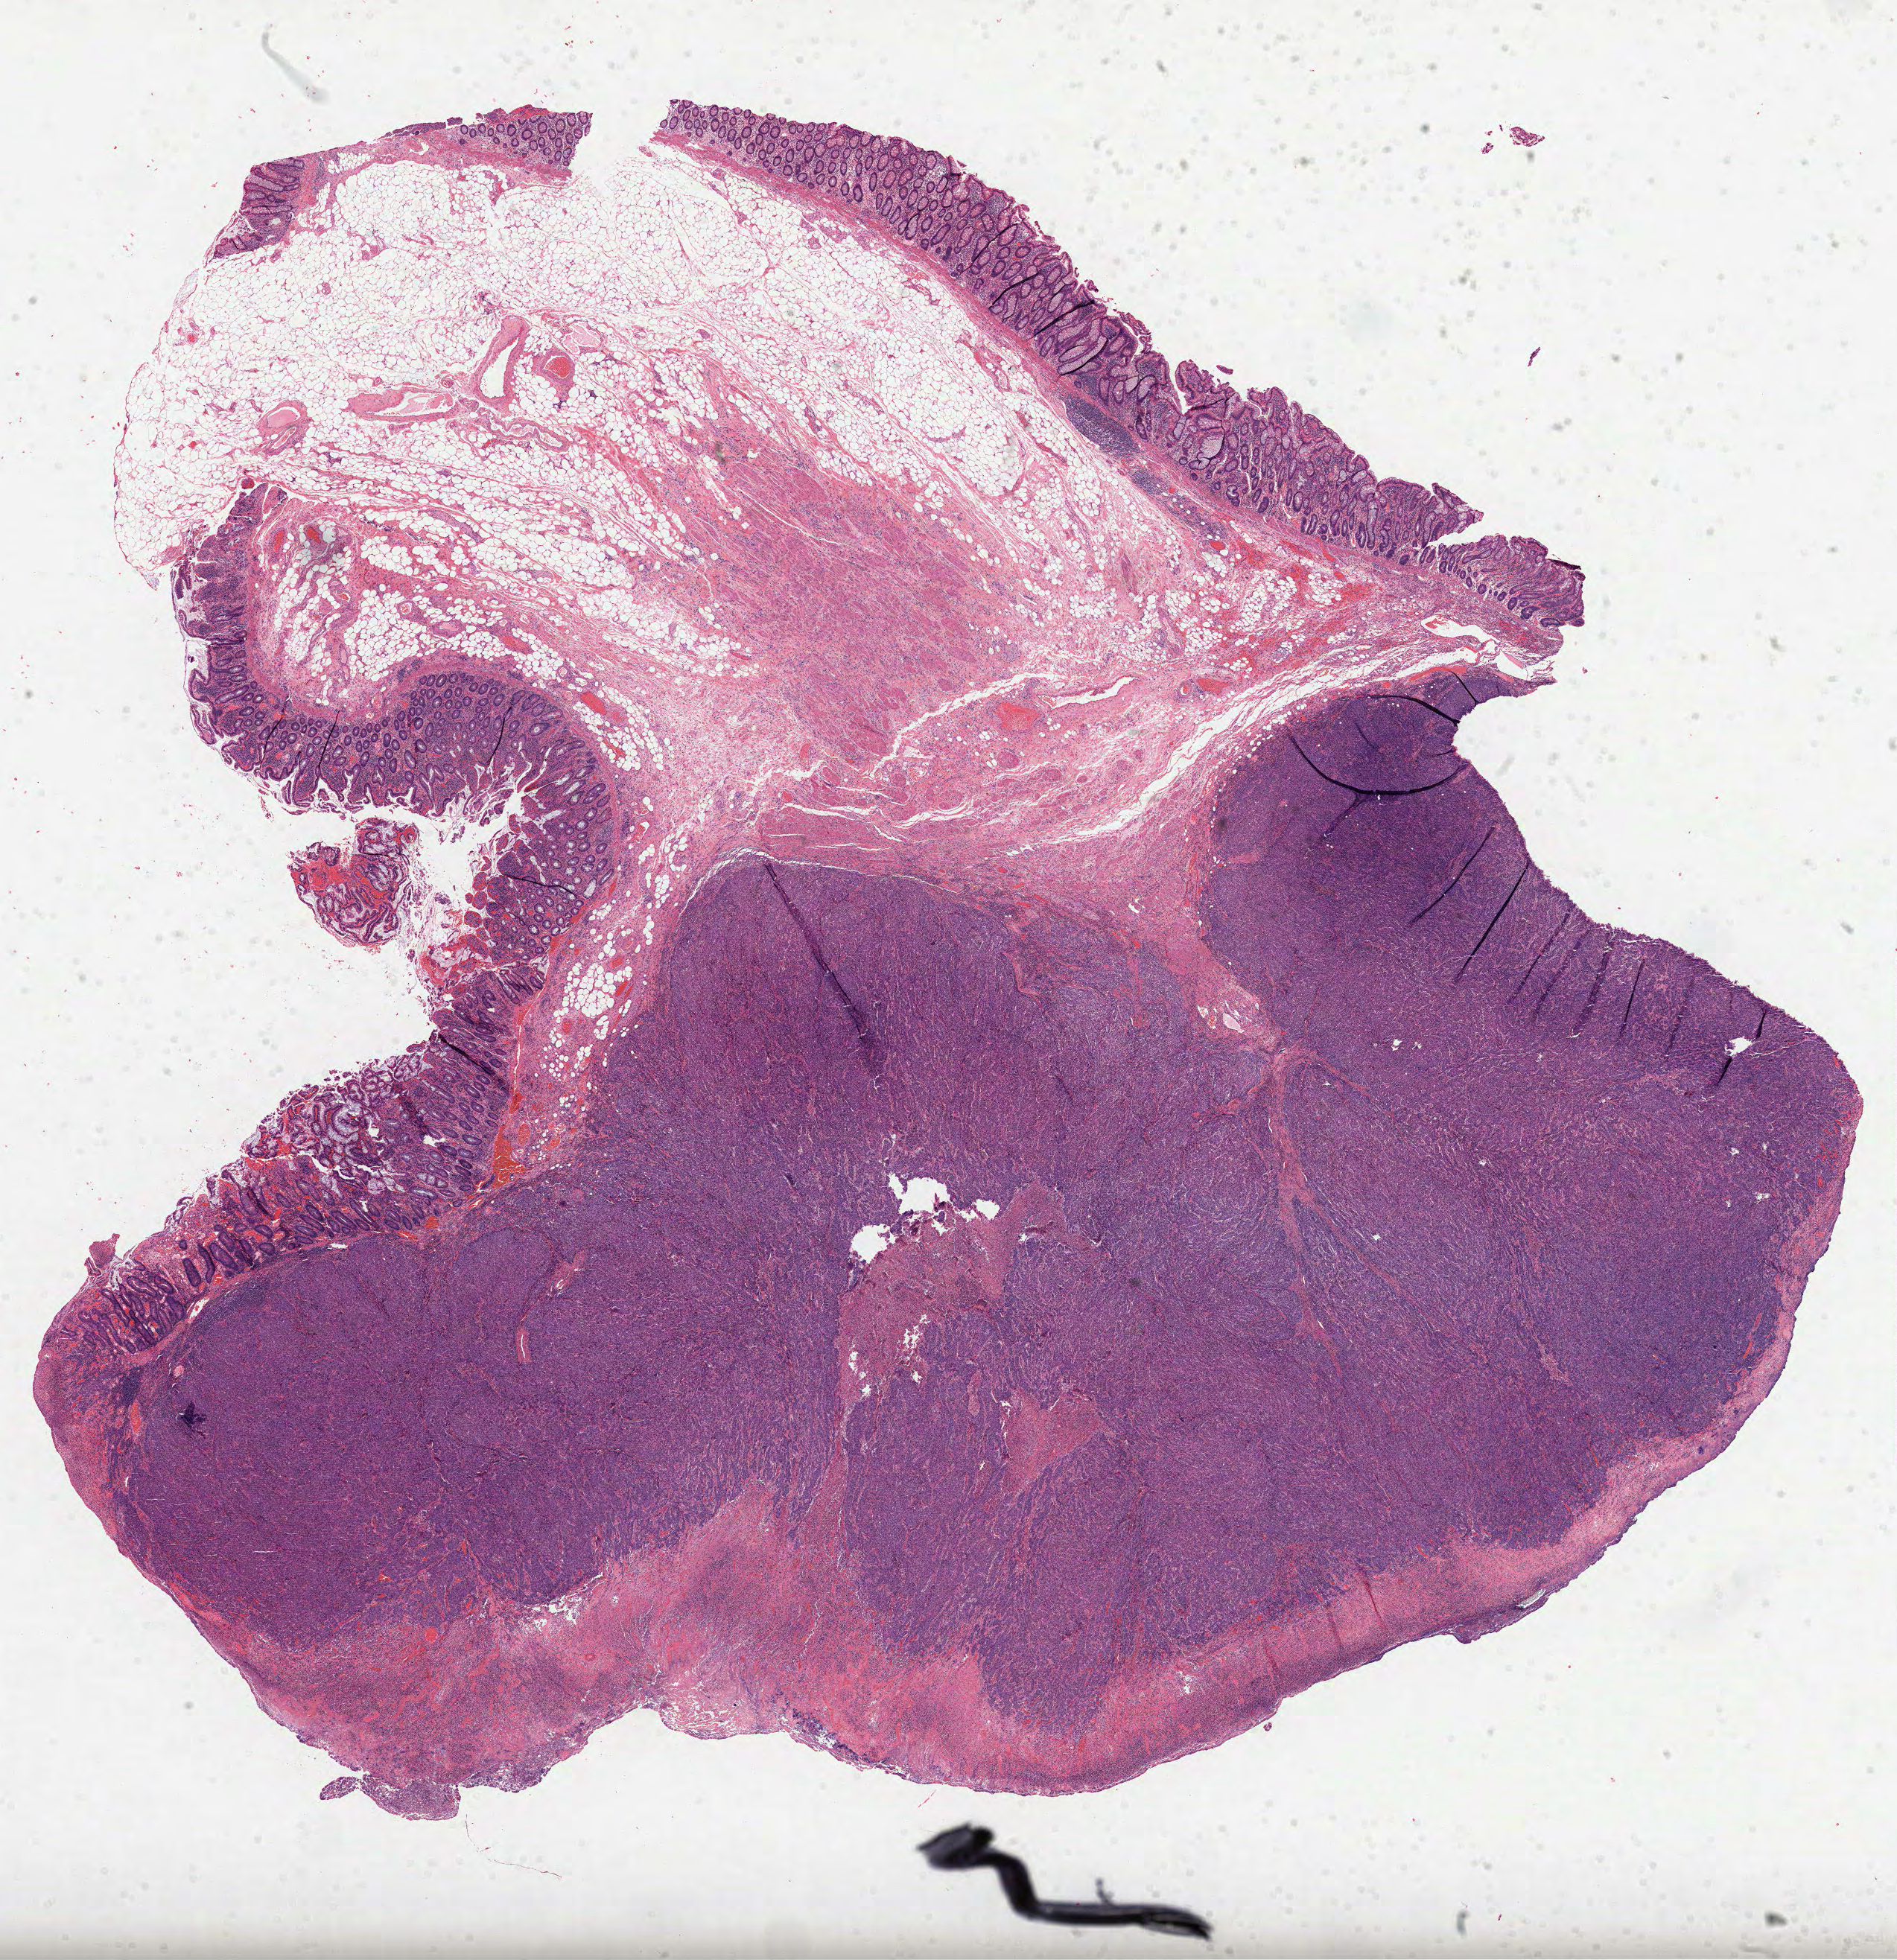
Digitized Hematoxylin and eosin (H&E) stained tissue section (whole slide) — shown as a low-resolution overview of the whole scanned area (about 20.5 x 21.2 mm). FFPE section. Primary tumour sample from the colon. Female, age 84 years at initial diagnosis.
• TNM: T4b N0 MX
• pathologic diagnosis: Adenocarcinoma, NOS (cecum)
• AJCC pathologic stage: IIB (6th edition)